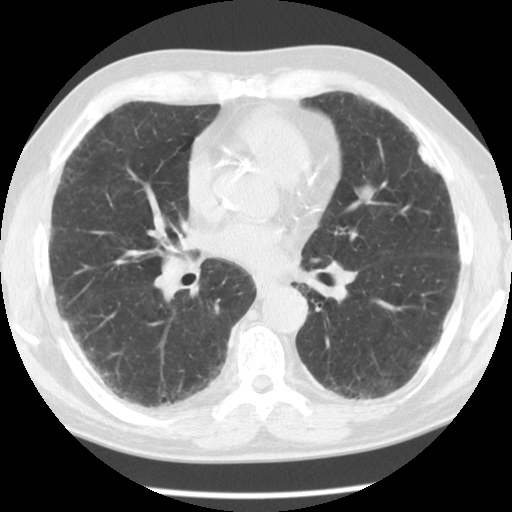
Low-dose screening chest CT, one axial slice. Position 55 of 113 along the scan axis. 120 kVp. Lung window (W 1500 / L -600 HU). 512 × 512 image matrix.
Structures marked on this image (outlined manually by an expert reader):
- lesion 1 (nodule, upper lobe of left lung): box from (x=355, y=185) to (x=373, y=204) px